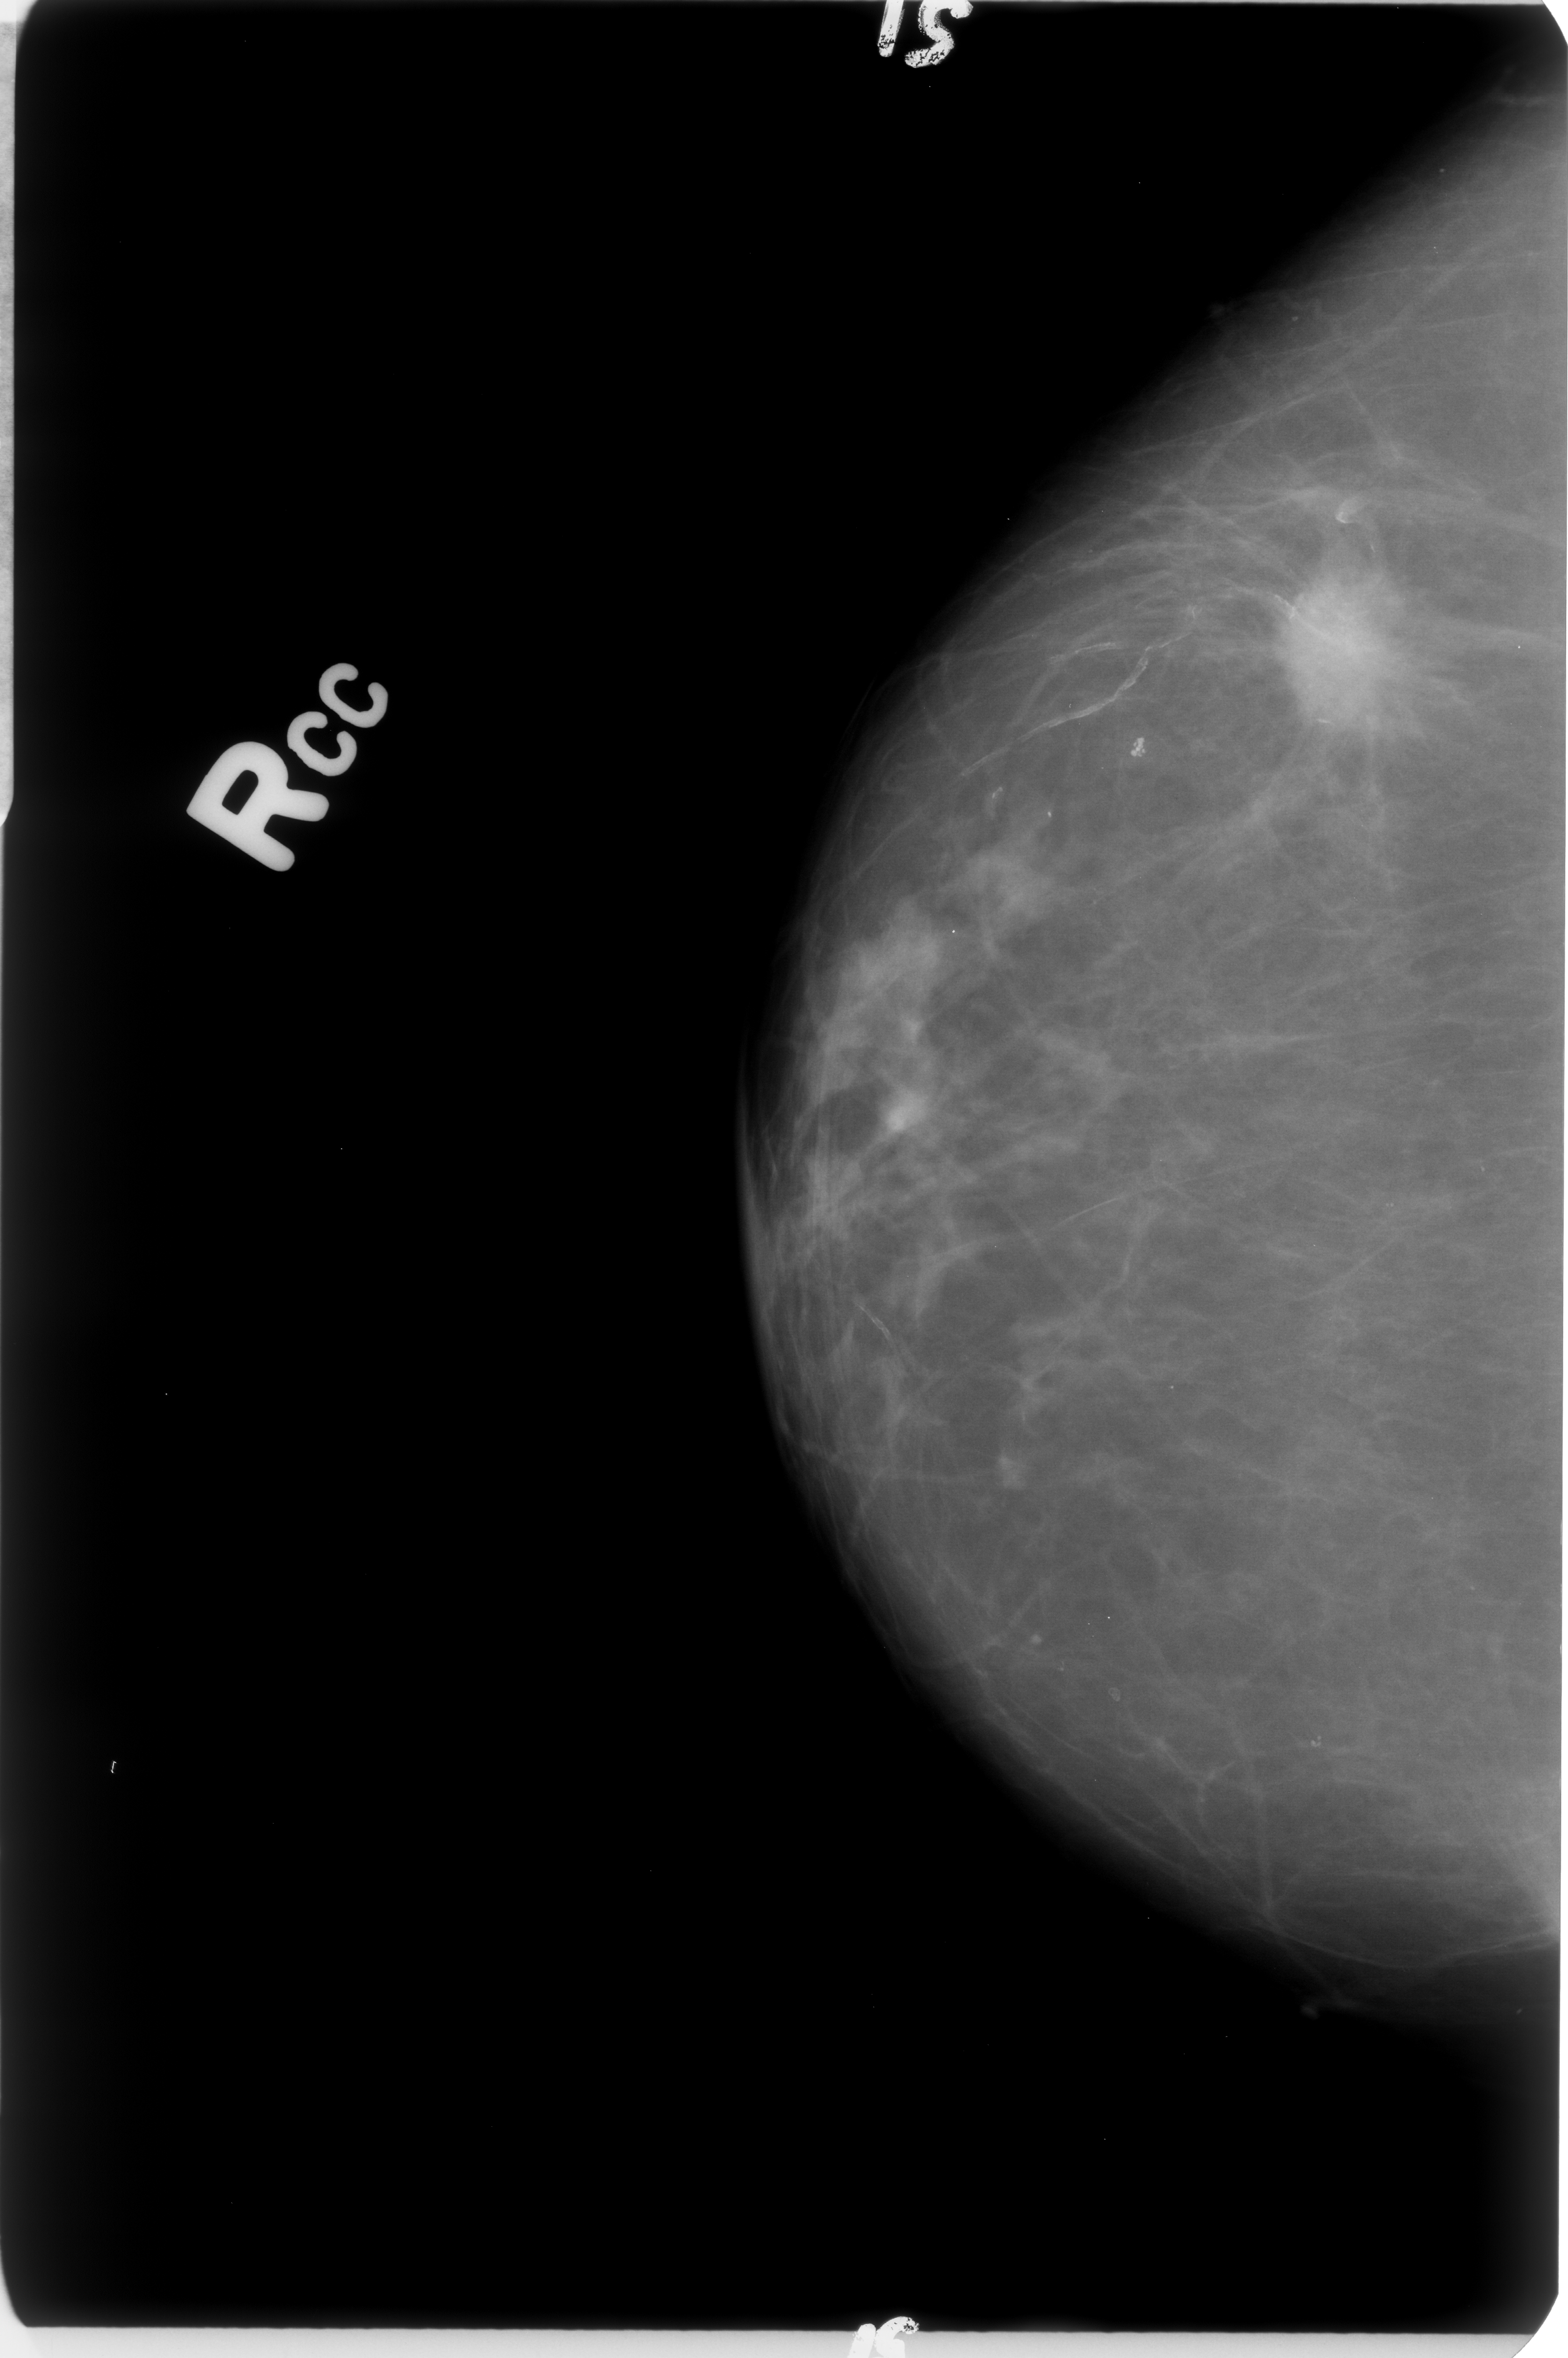
Mammogram (digitized film); right breast; CC view; BI-RADS breast density category 2 (scale 1–4).
- Finding: mass, shape irregular / architectural distortion, margins spiculated; BI-RADS assessment category 5; subtlety rating 5 on a 1 (subtle) to 5 (obvious) scale; pathology result (as recorded, not read from the image): malignant.